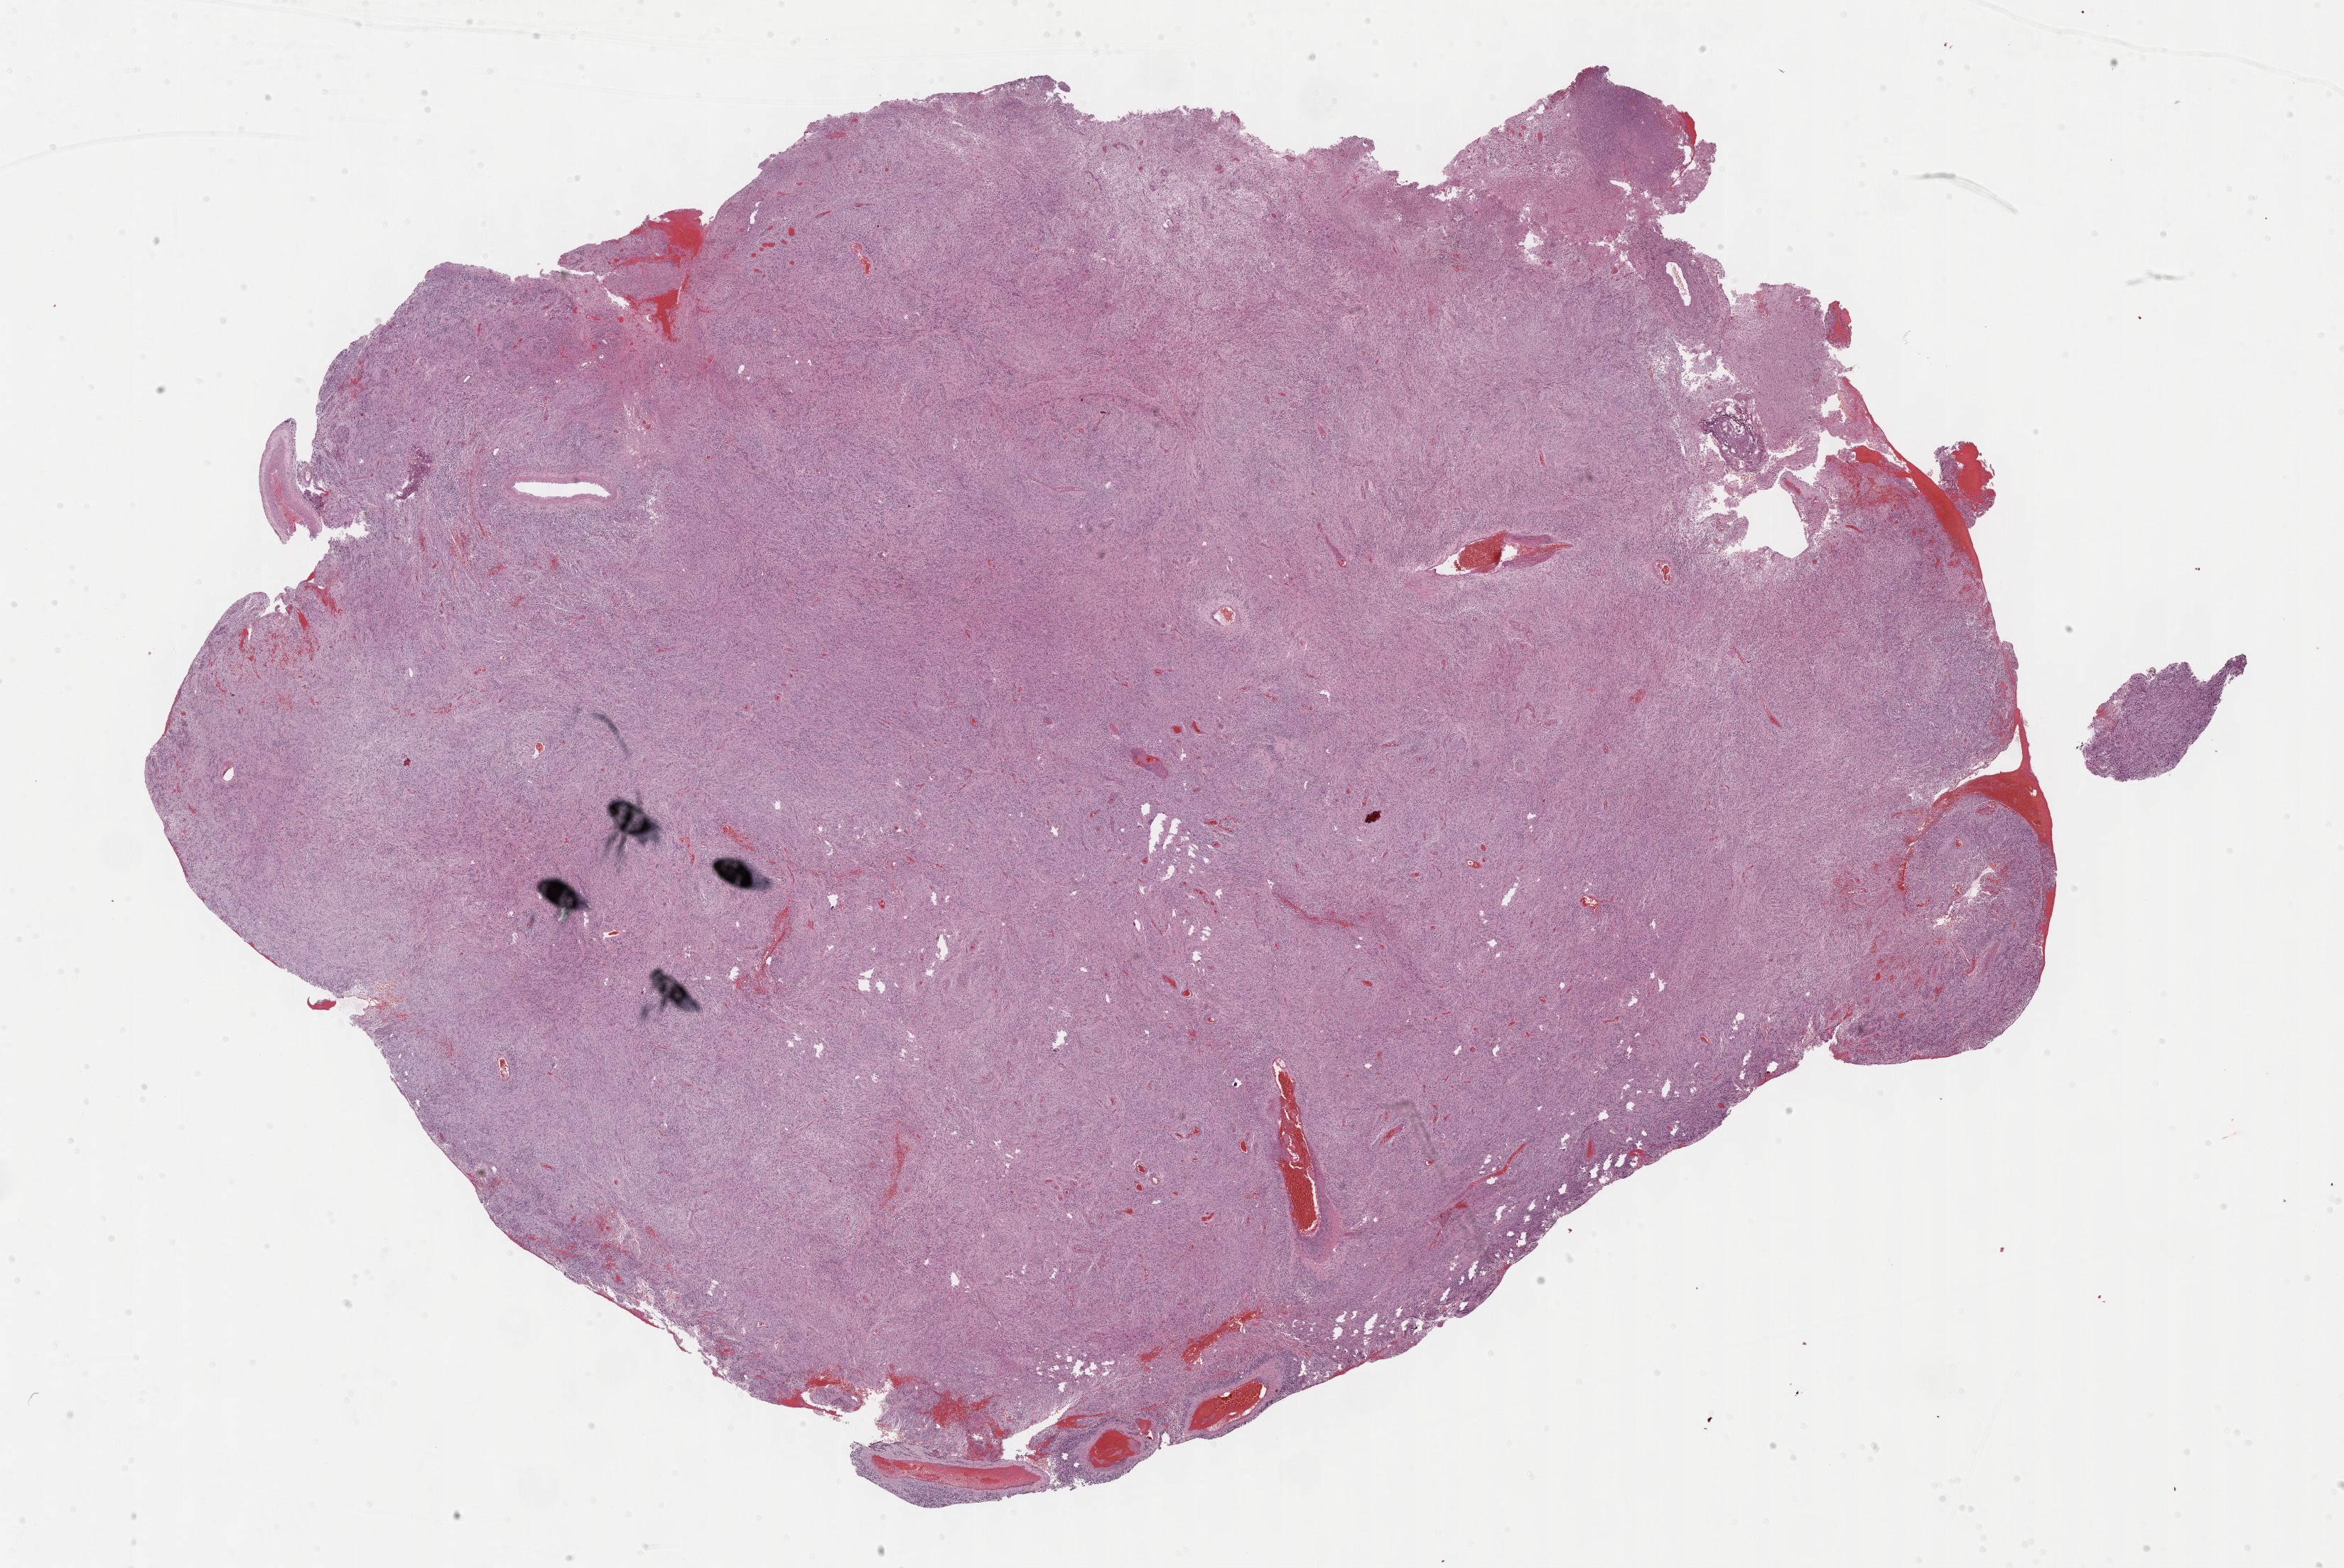
Whole-slide histology image, H&E — low-resolution overview of the scanned area, about 26.7 x 17.8 mm, formalin-fixed paraffin-embedded (FFPE) diagnostic section, primary tumour sample from the brain. Male patient; age at initial diagnosis 69 years.
- pathologic diagnosis: Glioblastoma